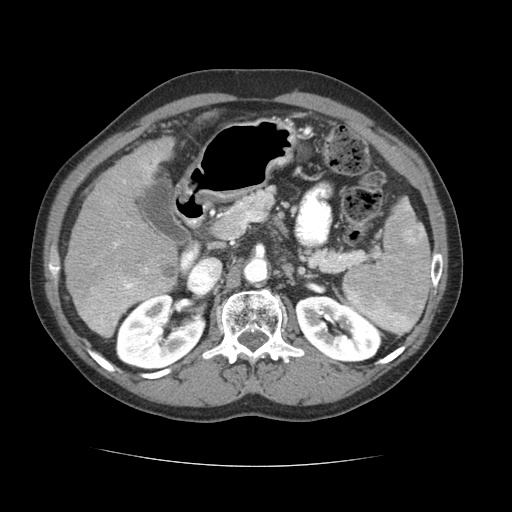
Contrast-enhanced abdominal CT (liver protocol), one axial slice. Slice 36 of 69 in the series (ordered by position). 120 kVp. Soft-tissue window (W 400 / L 40 HU). 2.5 mm slice thickness. 512 × 512 image matrix. From the clinical record (not read from this slice): diagnosis: hepatocellular carcinoma (patient treated with transarterial chemoembolisation; whether this scan precedes or follows treatment is not stated here); TNM stage (as recorded): Stage-II; Child-Pugh class: B; tumour differentiation: poorly differentiated; tumour size: 2.6 cm.
Outlined on this slice (semi-automatically segmented with operator editing):
- liver parenchyma outside the tumour (the mass and vessels are separate outlines, so this box may not span the whole liver): bounding box (x1, y1, x2, y2) in pixels: (64, 138, 178, 333)
- mass: (73, 262, 177, 338)
- liver vessels: (113, 158, 159, 270)